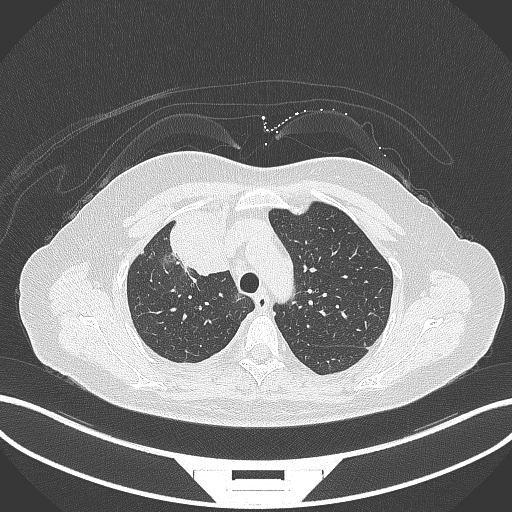
Chest CT, one axial slice. Slice 228 of 305 in the series (ordered by position). Reconstruction kernel B70f. 120 kVp. Lung window (W 1500 / L -600 HU). 1 mm slice thickness. 512 × 512 image matrix. Female patient, age 52 years. From the clinical record (not read from this slice): clinical TNM (as recorded): T3 N1 M1.
Structures marked on this image (rectangle marked by the reading radiologist):
- lung tumour (recorded histology: adenocarcinoma): bounding box <163,212,231,278> (left, top, right, bottom; pixels)